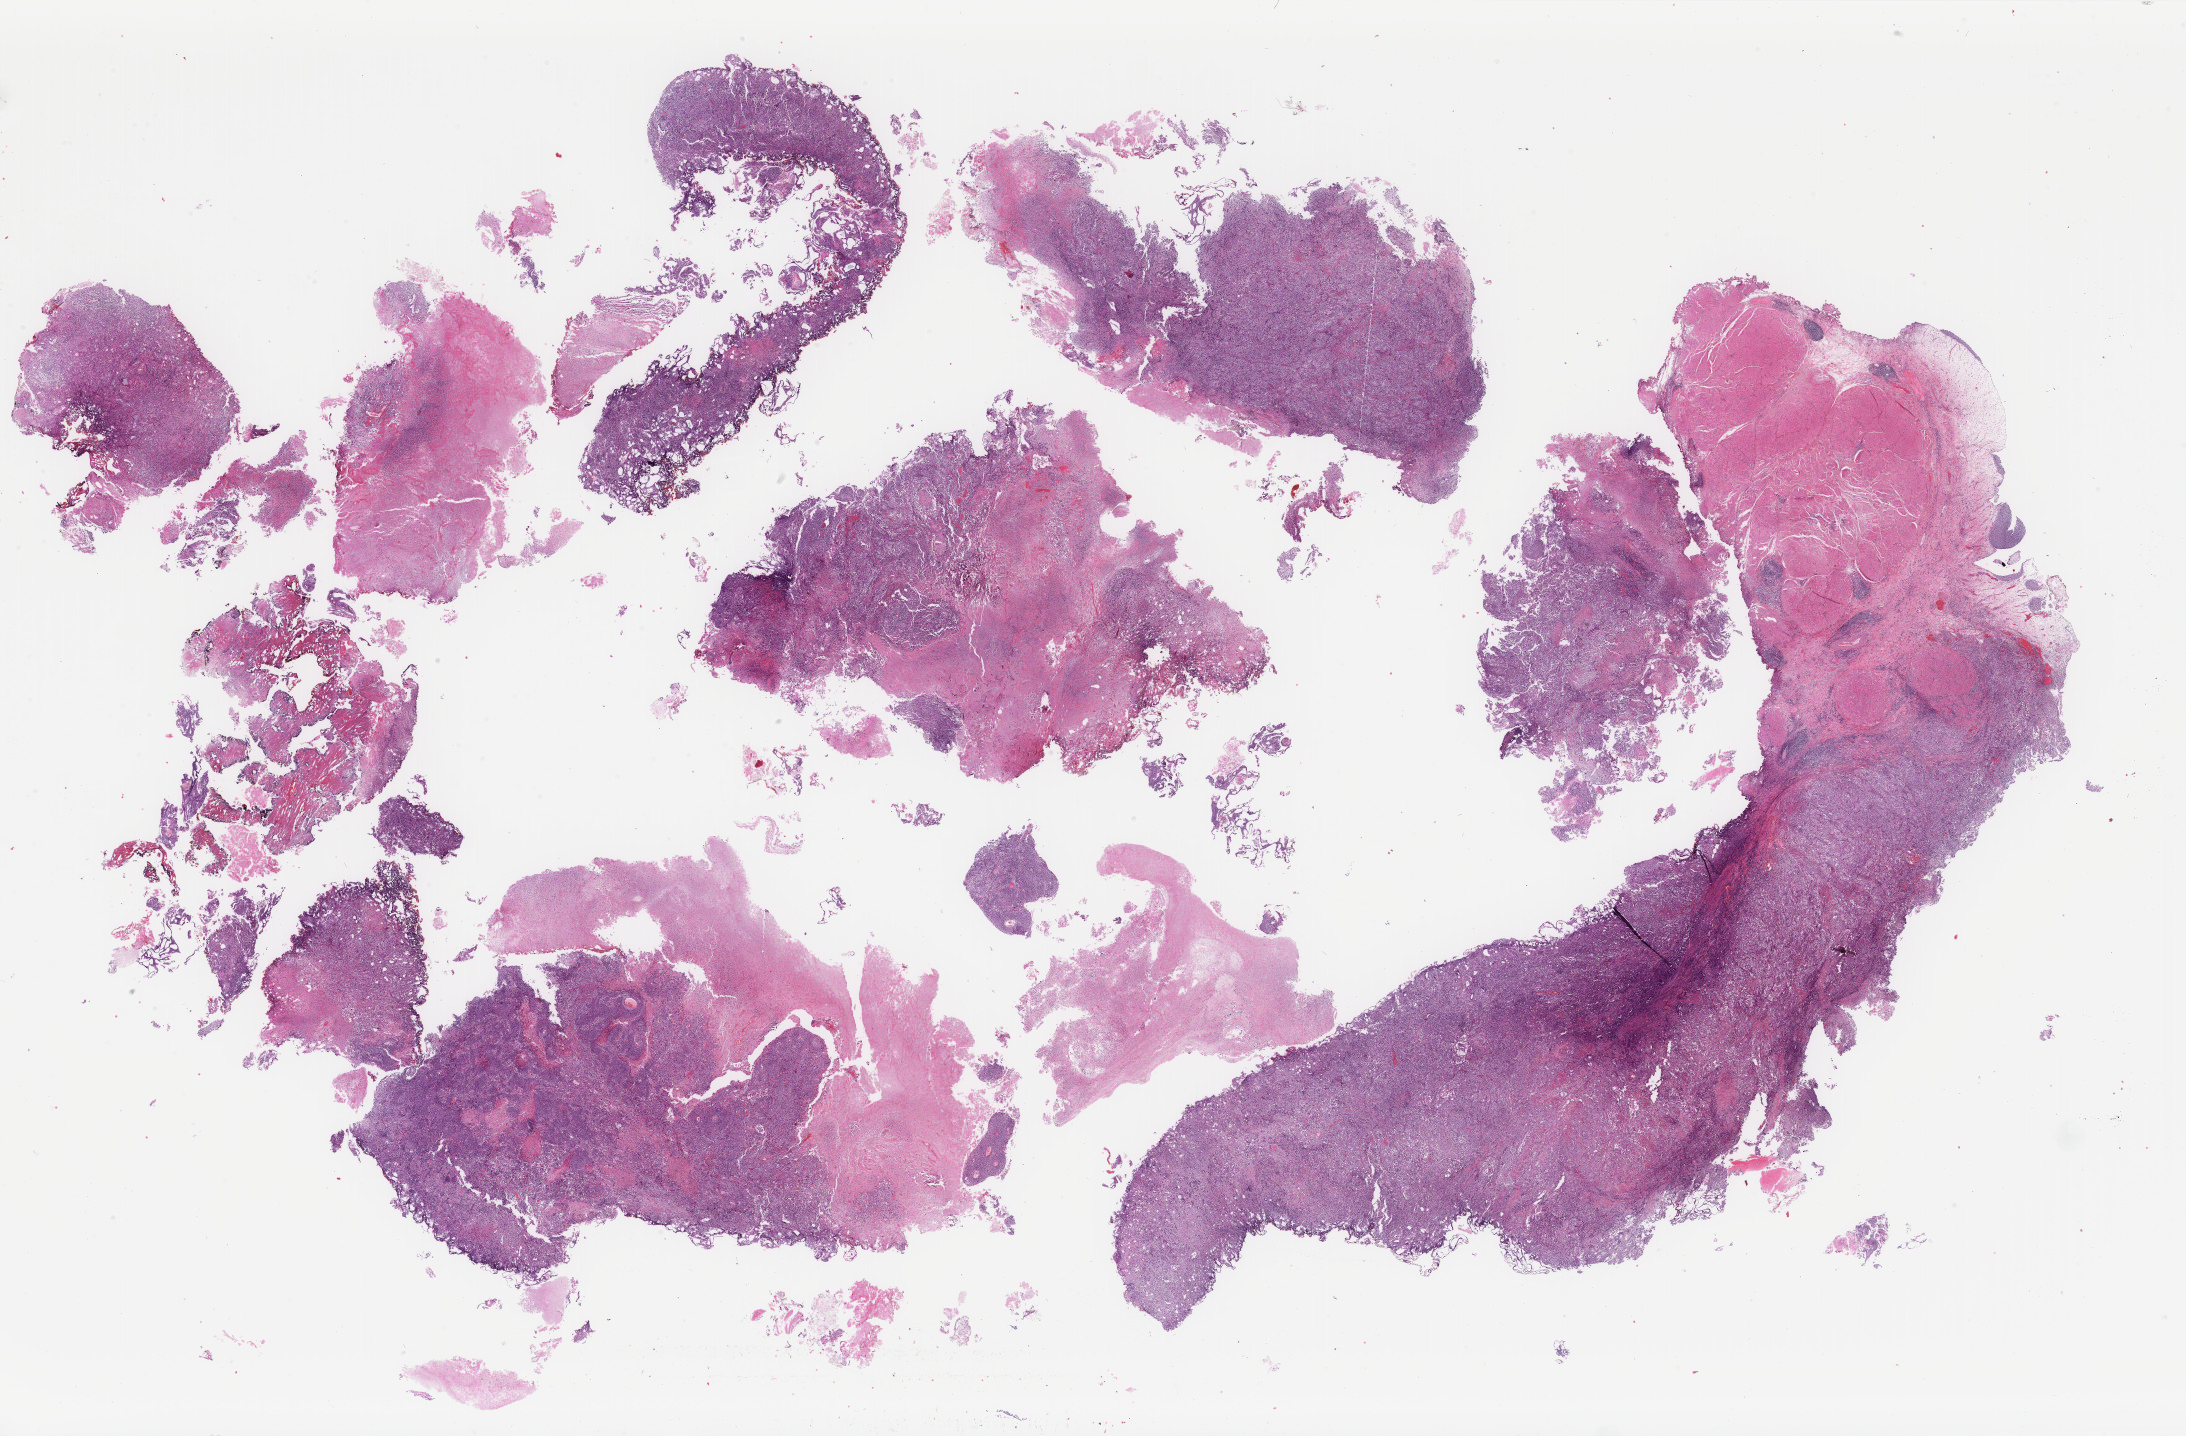
Whole-slide histology image, H&E, a low-resolution overview of the entire scanned area, about 34.7 x 22.8 mm (acquisition: 40x scan); FFPE section; primary tumour sample from the bladder. Male patient; age at initial diagnosis 50 years. Histologic grade: high grade.
* AJCC pathologic stage: II (6th edition)
* pathologic diagnosis: Transitional cell carcinoma